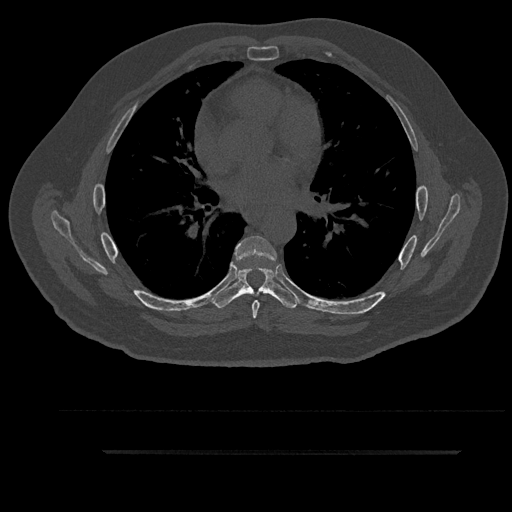
CT including the spine, one axial slice; position 550 of 797 along the scan axis; reconstruction kernel Br40s/3; bone window (W 1800 / L 400 HU); 0.5 mm slice thickness; 512 × 512 image matrix. Male patient, age 63 years. From the clinical record (not read from this slice): primary cancer: renal; vertebrae with lytic lesions (as recorded): T8.
Structures marked on this image (semi-automatic segmentation, software-assisted and operator-edited):
- T5 vertebra: bounding box <261,288,266,291> (left, top, right, bottom; pixels)
- T6 vertebra: <235,236,277,319>
- T7 vertebra: <213,266,299,308>